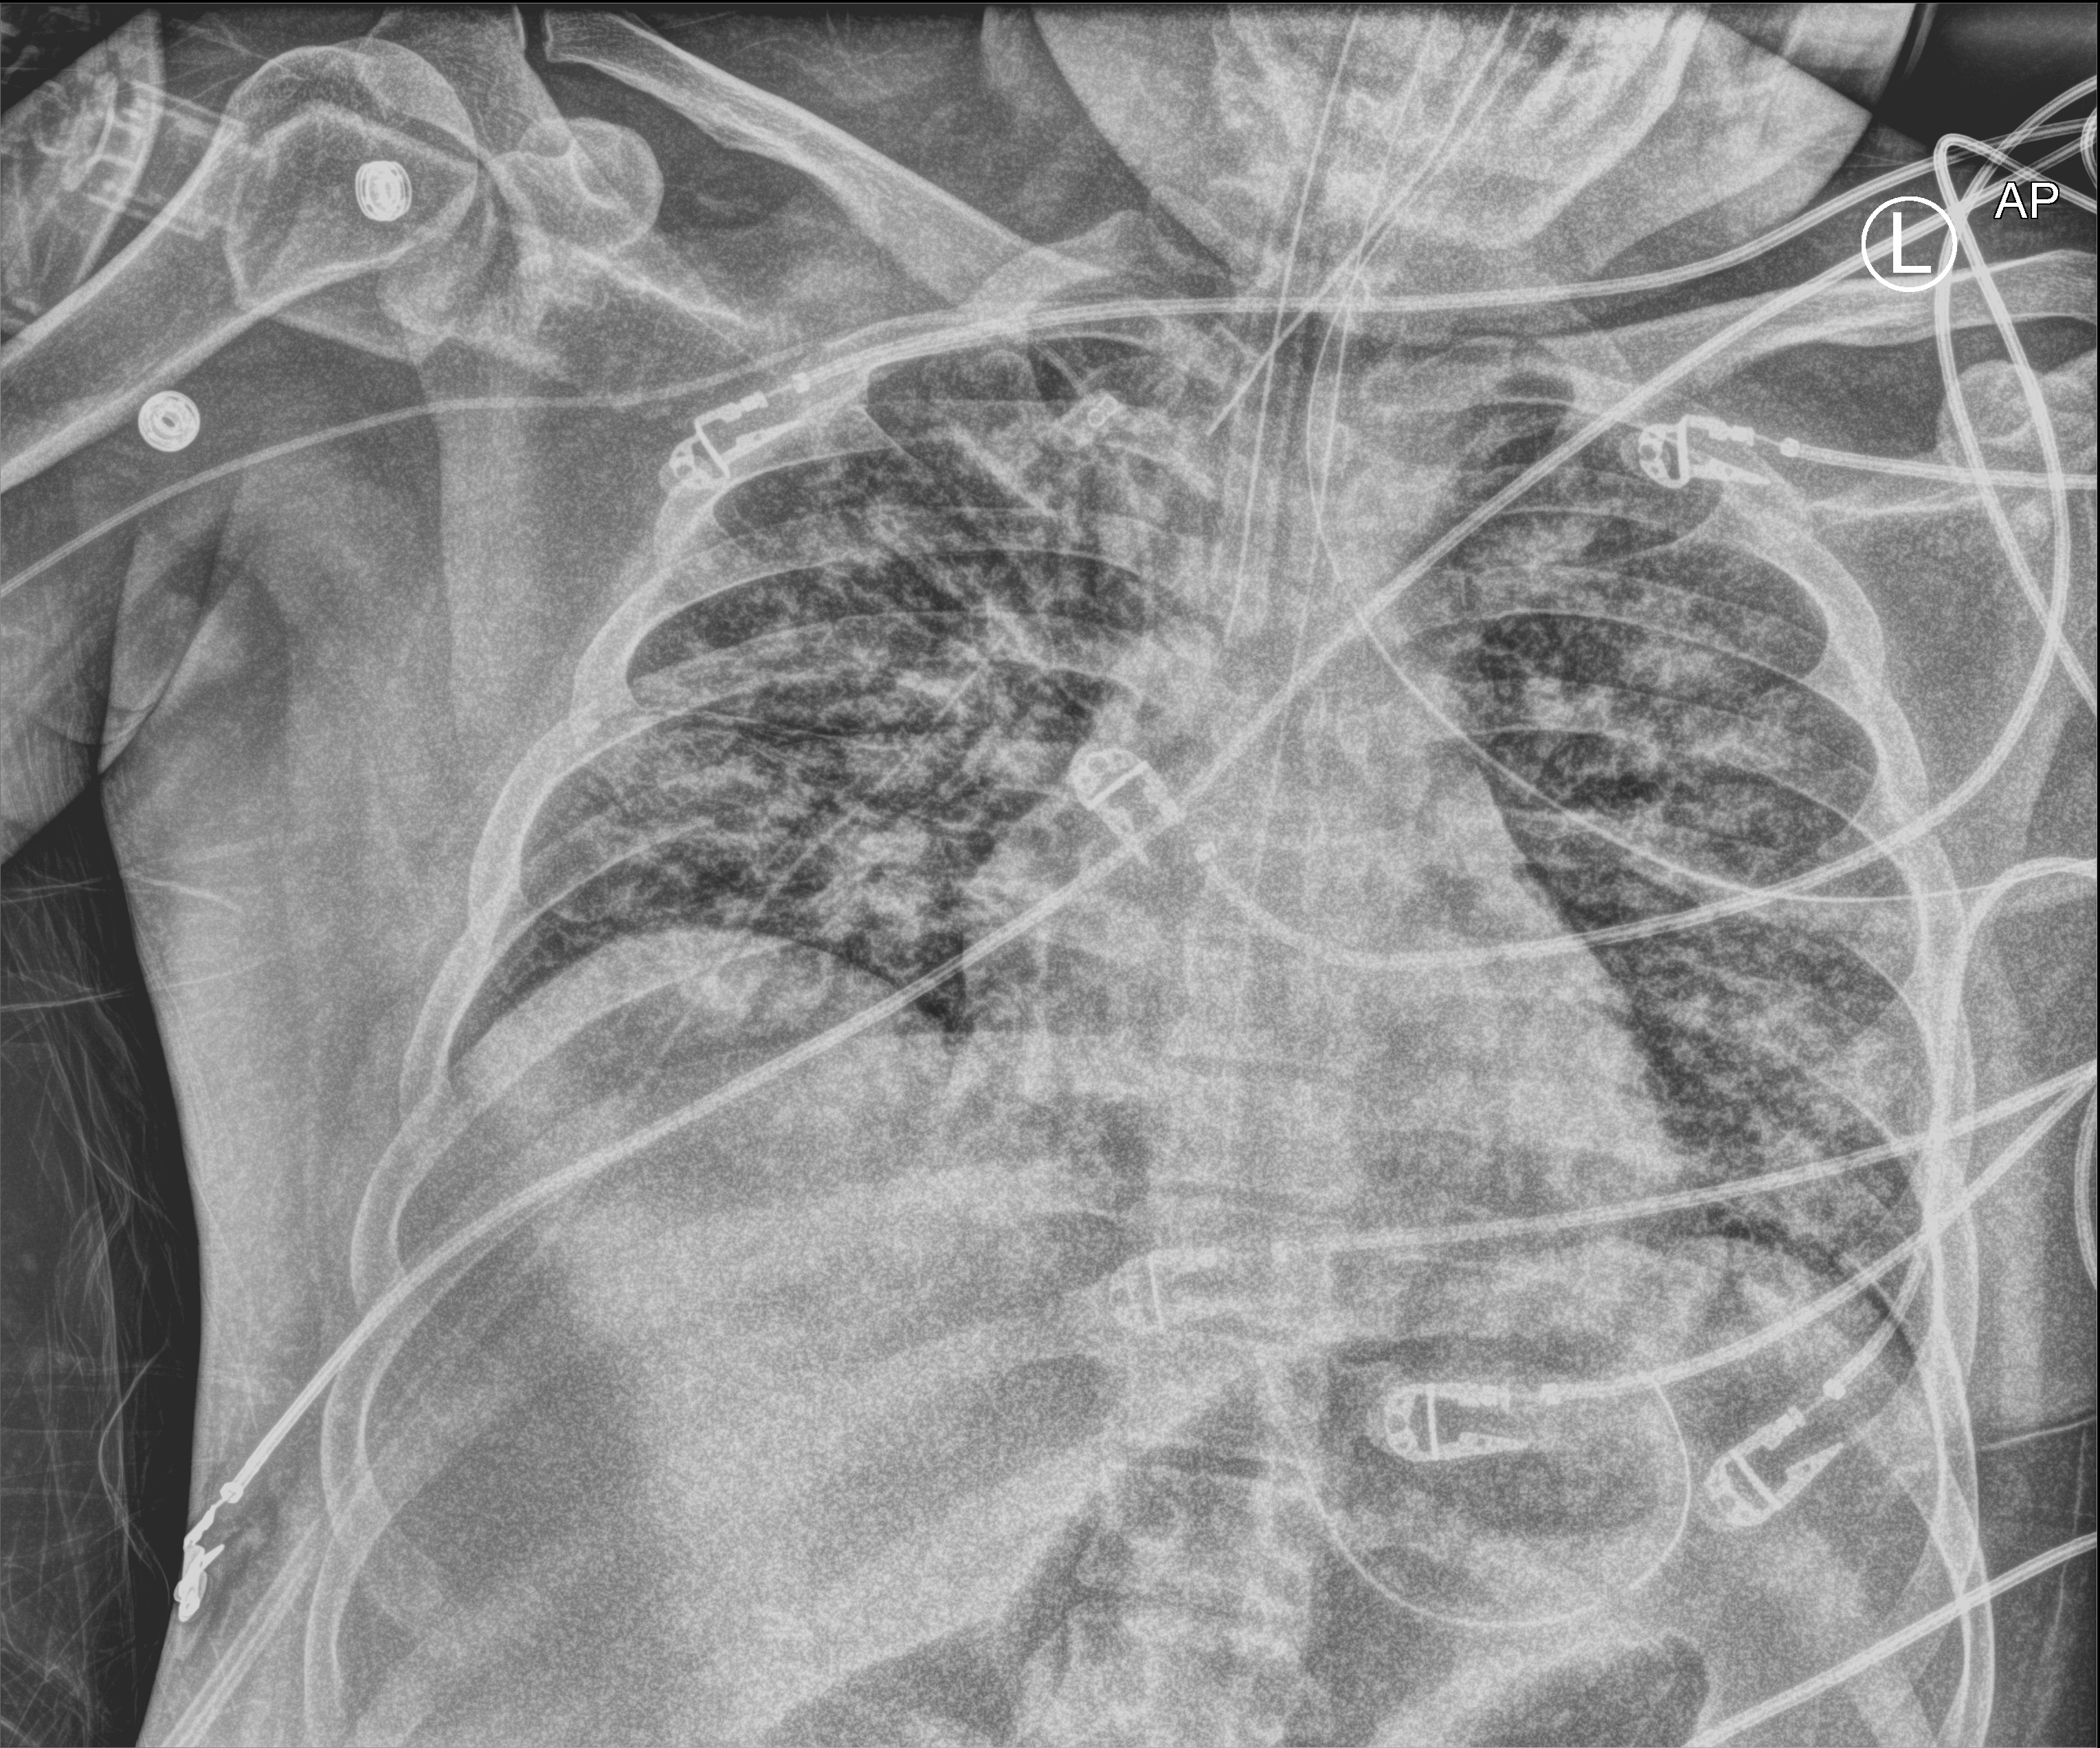
Portable chest radiograph, anteroposterior (AP) projection. Patient hospitalised with COVID-19; male, aged 18–59 years.
Hospital-stay facts (about this admission, not read from this image; timing relative to this image not recorded):
- length of hospital stay: 44 days
- smoking status (admission record): former
- other chronic lung disease (admission record): no